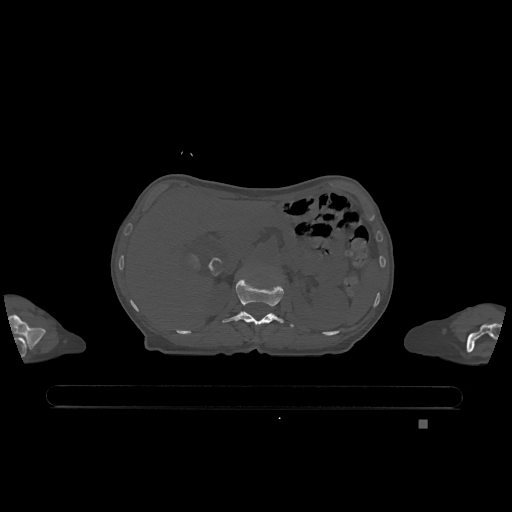
CT including the spine, one axial slice; slice 470 of 1317 in the series (ordered by position); bone window (W 1800 / L 400 HU); 0.5 mm slice thickness; 512 × 512 image matrix, field of view 500 × 500 mm. Female patient, age 74 years. From the clinical record (not read from this slice): primary cancer: lung.
Outlined on this slice (semi-automatic segmentation, software-assisted and operator-edited):
- L1 vertebra: bounding box (x1, y1, x2, y2) in pixels: (222, 278, 294, 328)